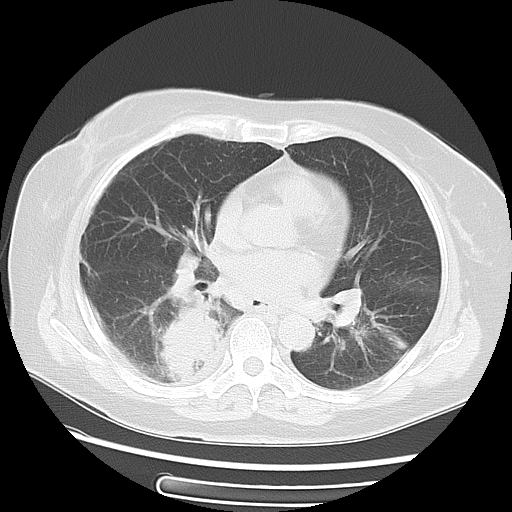
Chest CT, one axial slice; position 30 of 57 along the scan axis; reconstruction kernel LUNG; lung window (W 1500 / L -600 HU); 5 mm slice thickness; 512 × 512 image matrix, field of view 350 × 350 mm. Female patient, age 69 years. From the clinical record (not read from this slice): clinical TNM (as recorded): T2 N1 M1a.
Annotated regions visible in this slice (rectangle marked by the reading radiologist):
- lung tumour (recorded histology: adenocarcinoma): box from (x=154, y=296) to (x=228, y=392) px